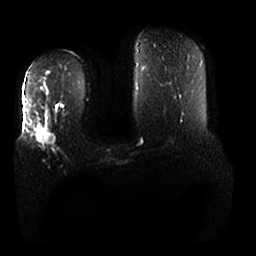
Breast MRI, one axial slice. Position 10 of 25 along the scan axis. Diffusion-weighted series; image 2 of 4 stored at this slice position (different b-values; order by instance number). 1.5 T. 4 mm slice thickness. 256 × 256 image matrix, field of view 380 × 380 mm. Female patient.
Annotated regions visible in this slice (outlined manually by an expert reader):
- tumour on diffusion-weighted imaging: bounding box [x1, y1, x2, y2] px = [36, 126, 55, 145]